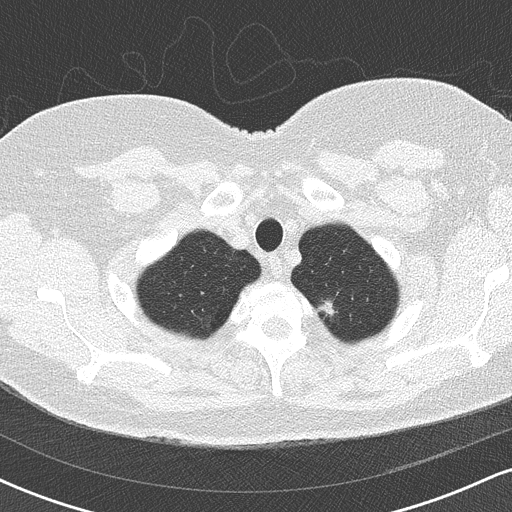
Low-dose screening chest CT, axial slice, third screening round (two years after baseline), lung window (W 1500 / L -600 HU), lung (sharp) reconstruction kernel (B50f), 512 × 512 image matrix, field of view 320 × 320 mm. Female, age 60 years at enrolment. Former smoker at enrolment.
Expert reader's lesion annotation, bounding box [x1, y1, x2, y2] px = [299, 287, 352, 334]. Screening reader's record for this exam (one nodule recorded; not confirmed to be the boxed lesion): non-calcified nodule or mass ≥4 mm, left upper lobe, 10 × 10 mm, soft tissue attenuation, pre-existing on the prior screen: yes. Official screen result: positive, no significant change: stable abnormalities potentially related to lung cancer, unchanged since the prior screening exam.